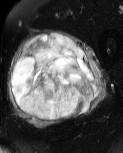
MRI of an extremity soft-tissue mass, one axial slice; T2-weighted fat-saturated; MR volume resampled by the dataset authors to the PET/CT grid (not the native acquisition matrix); 123 × 153 image matrix. Male patient. Case-level facts recorded for this patient, not image findings: histological type: pleiomorphic liposarcoma; grade: high; site of the primary tumour: left thigh.
Annotated regions visible in this slice (expert contour drawn on MRI and transferred to this co-registered scan by the dataset authors):
- gross tumour volume including surrounding oedema: bounding box <8,29,107,128> (left, top, right, bottom; pixels)
- gross tumour volume (mass): <11,34,99,121>